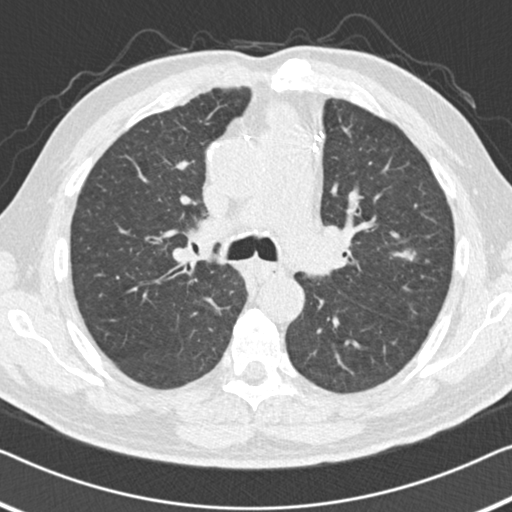
Low-dose screening chest CT, one axial slice; slice 100 of 155 in the series (ordered by position); 120 kVp; lung window (W 1500 / L -600 HU); 2 mm slice thickness; 512 × 512 image matrix, field of view 332 × 332 mm.
Annotated regions visible in this slice (expert manual segmentation):
- lesion 1 (tumor, upper lobe of left lung): box from (x=391, y=249) to (x=417, y=262) px